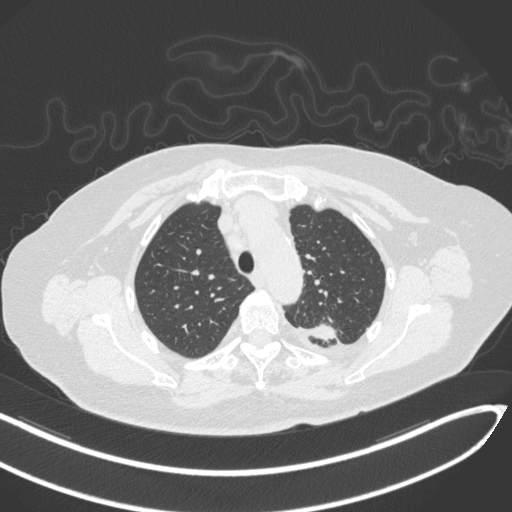
Chest CT, one axial slice. Slice 246 of 270 in the series (ordered by position). Reconstruction kernel B31f. 120 kVp. Lung window (W 1500 / L -600 HU). 512 × 512 image matrix, field of view 400 × 400 mm. Patient: female, 76 years. Case-level facts recorded for this patient, not image findings: clinical TNM (as recorded): T1c N0 M0.
Annotated regions visible in this slice (bounding box drawn by a radiologist):
- lung tumour (recorded histology: adenocarcinoma): bounding box (x1, y1, x2, y2) in pixels: (307, 318, 339, 347)